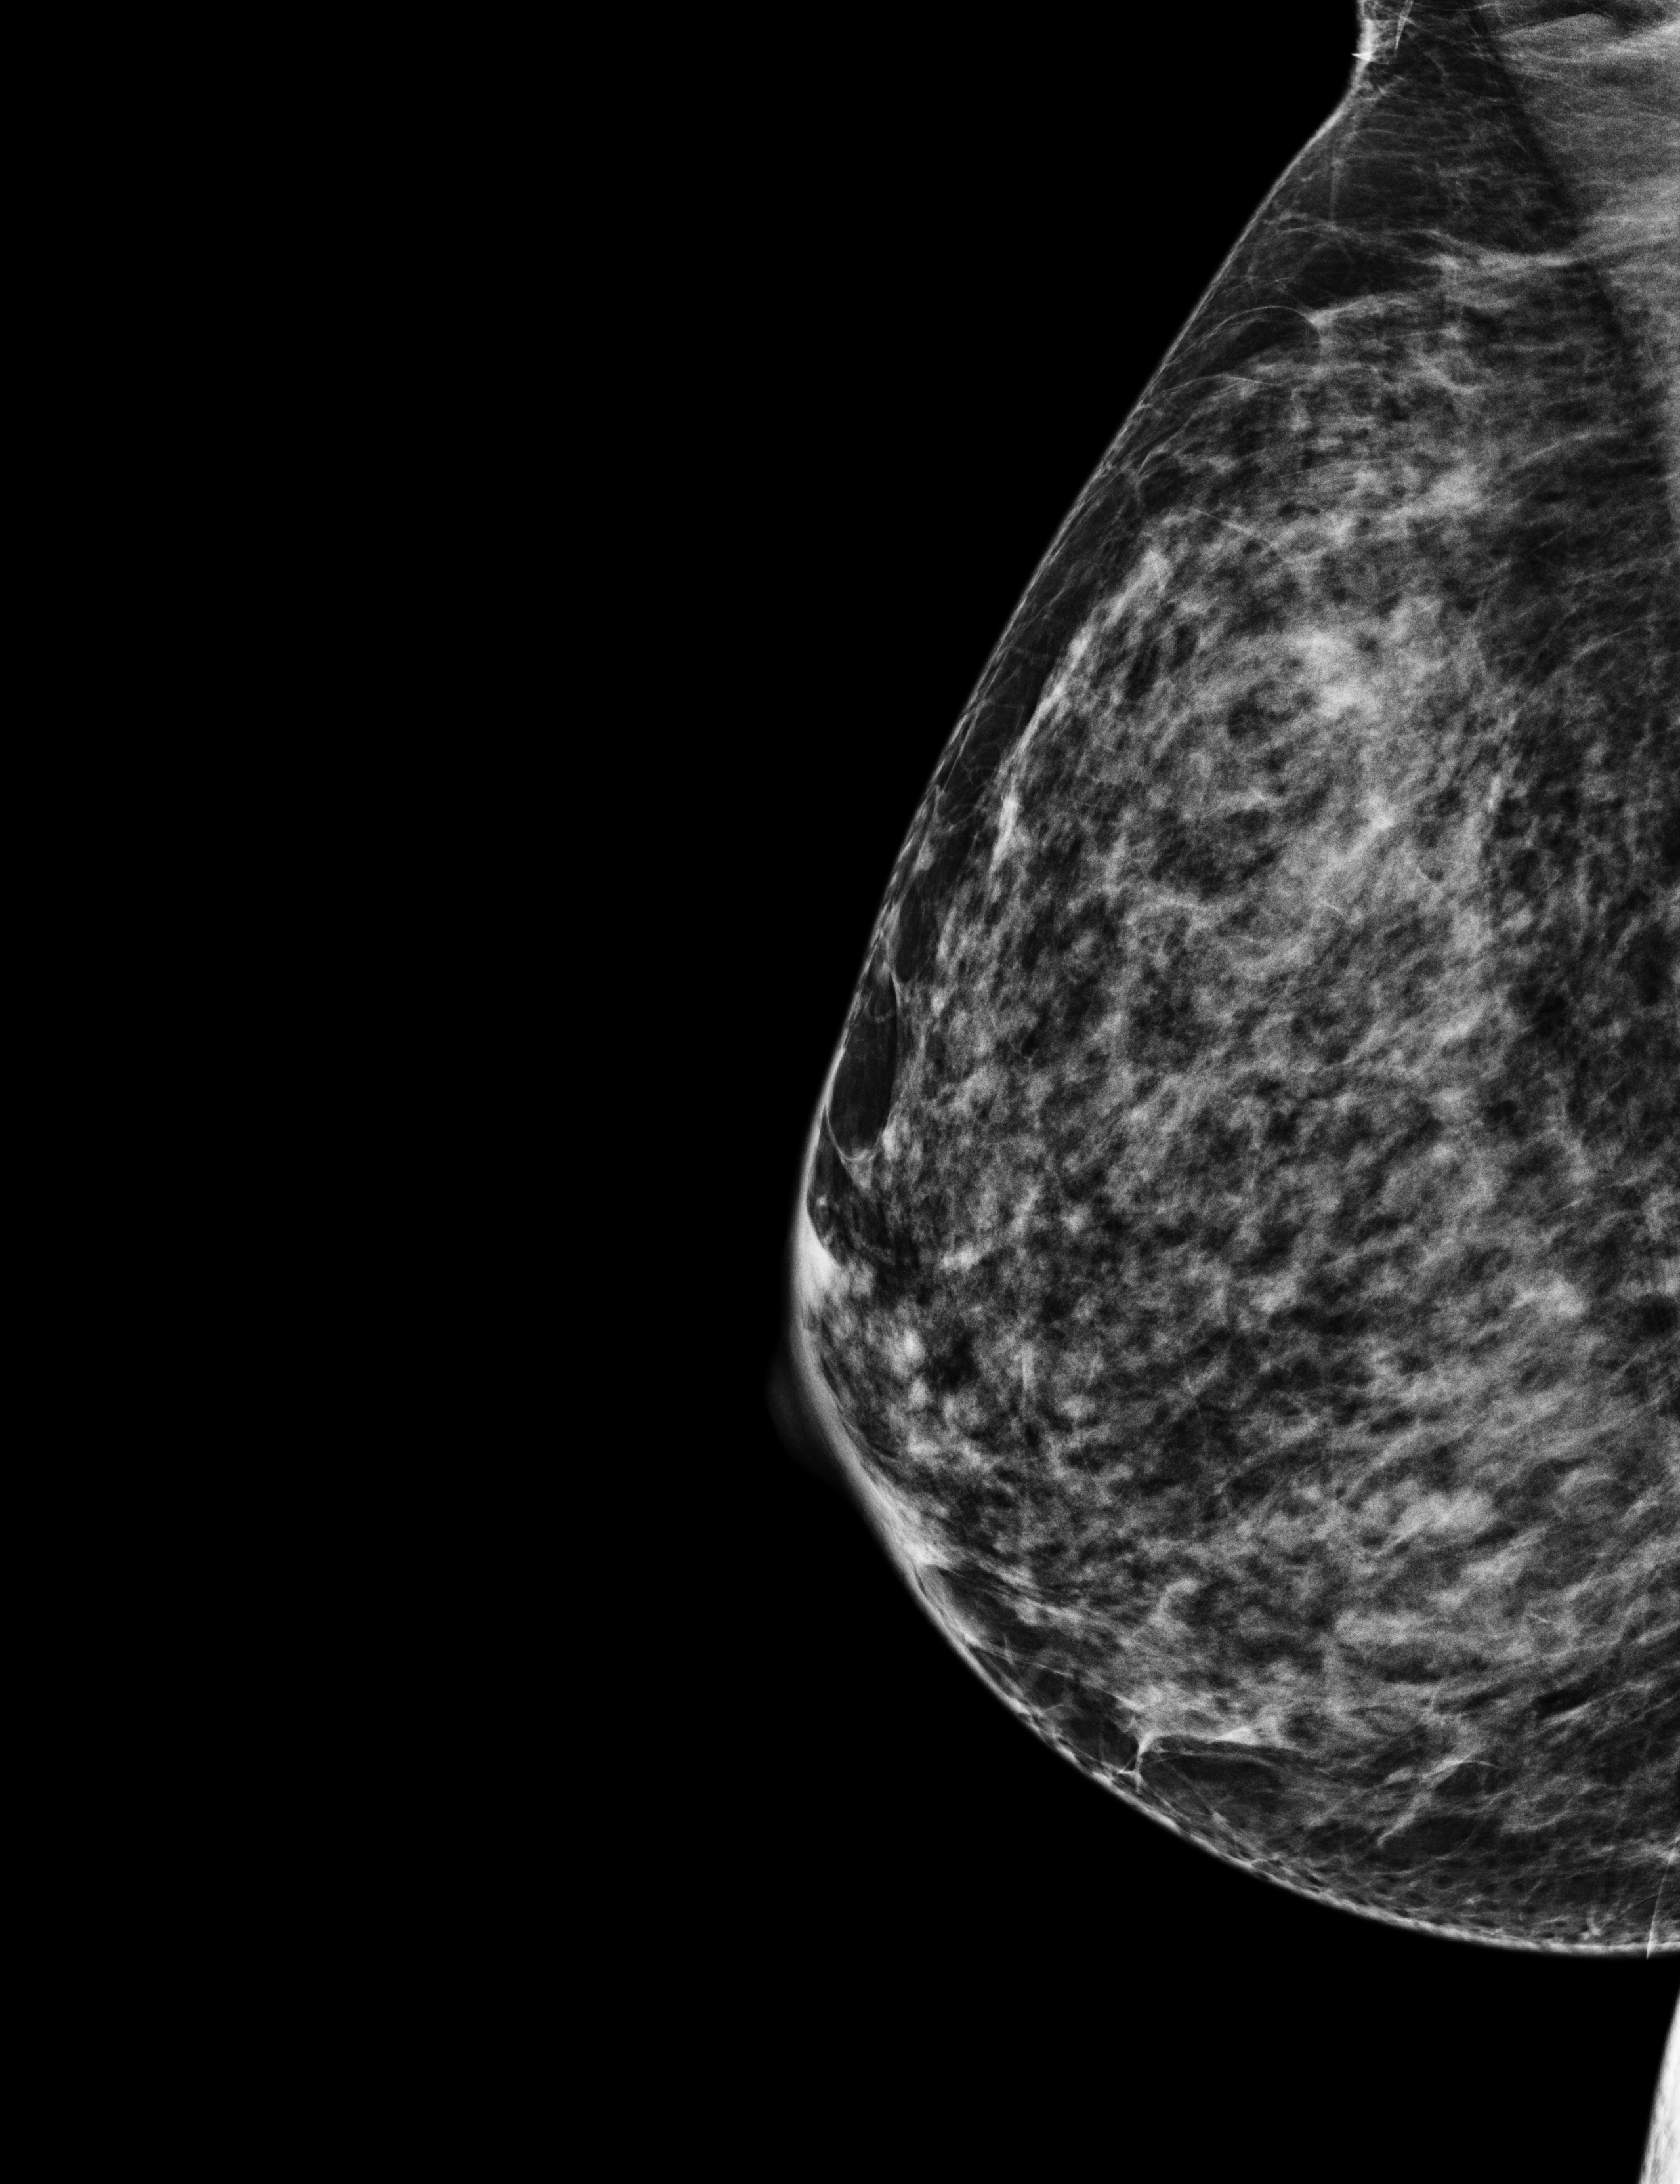
Annual screening mammography examination; compressed breast thickness 45 mm. Patient: female, 50 years.
Image type: full-field digital mammogram. Breast: right. Projection: laterally exaggerated craniocaudal (XCCL) view.